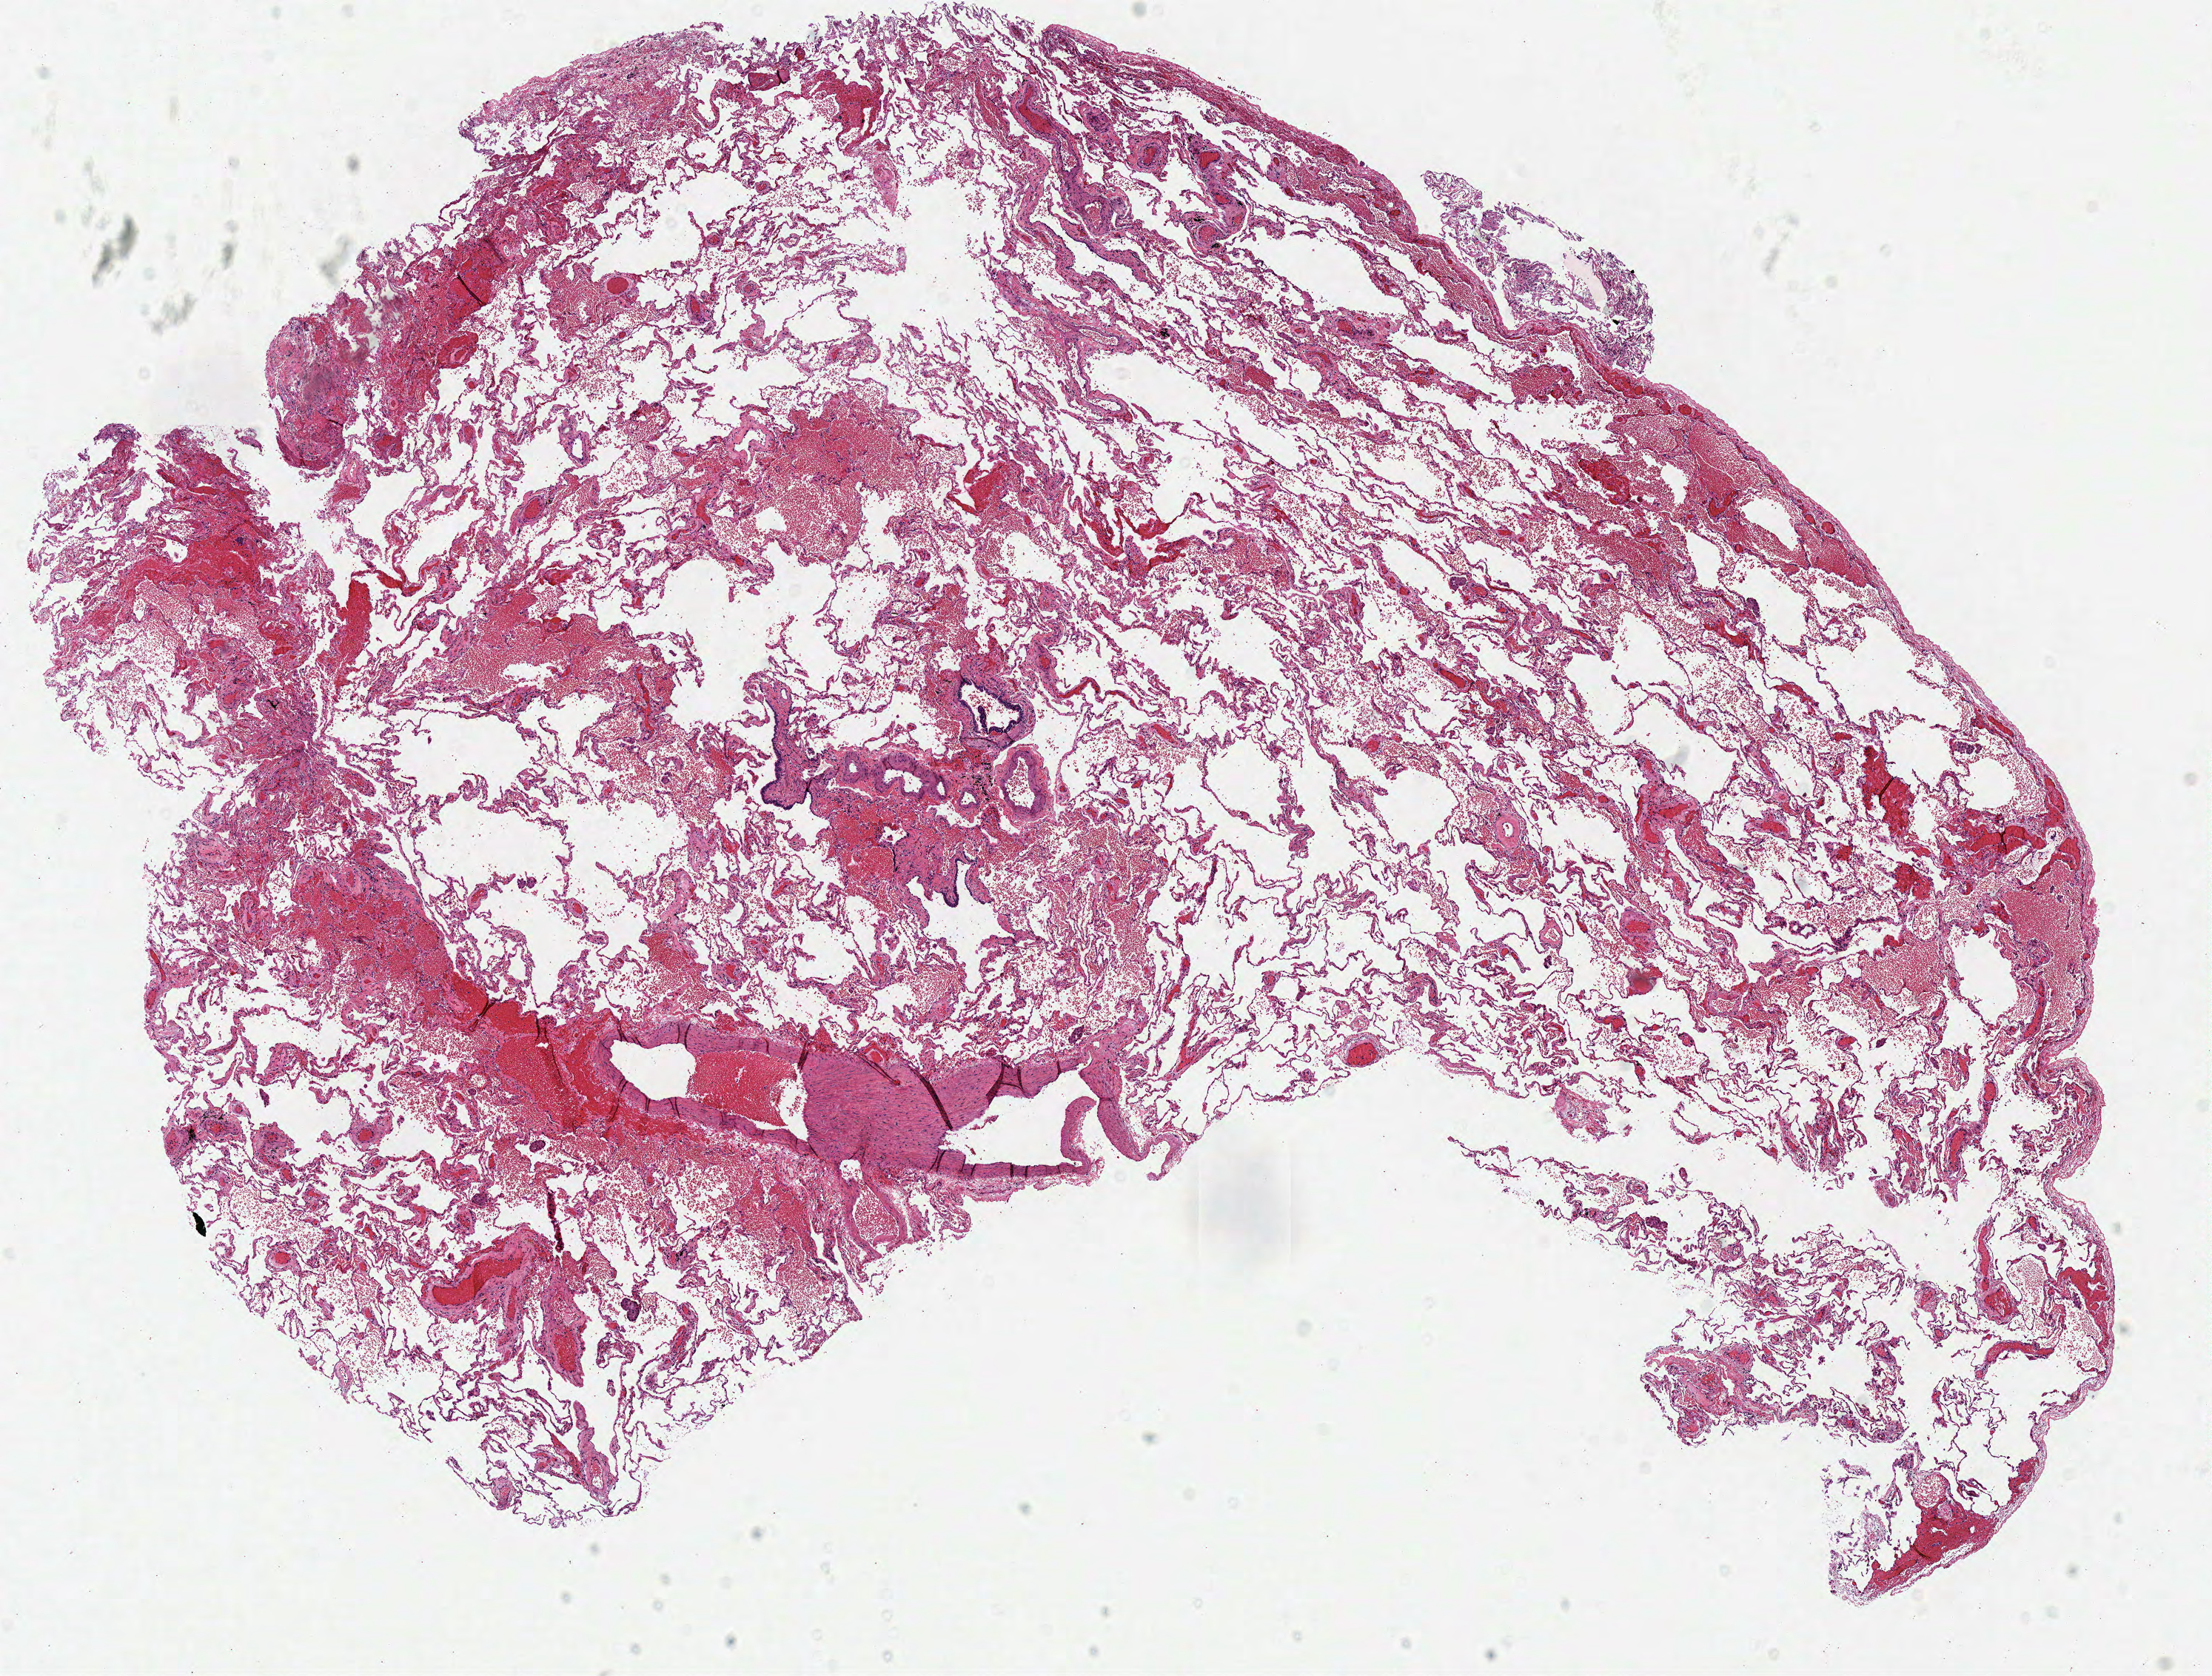
Hematoxylin and eosin (H&E) stained whole-slide image — whole scanned area (about 11.7 x 8.9 mm, acquisition: 40x scan) shown as a low-resolution overview, frozen section, lung, solid tissue normal (non-tumour tissue) sample. Patient: female, age at initial diagnosis 72 years.
• this section: solid tissue normal (non-tumour) sample from the same patient
• patient diagnosis: Adenocarcinoma, NOS (upper lobe, lung)